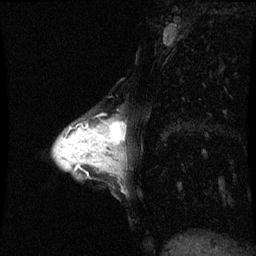
Breast MRI (dynamic contrast-enhanced), one sagittal slice; dynamic contrast-enhanced series, image 2 of 3 at this slice position (ordered by acquisition); 1.5 T; TE 4.2 ms, TR 8.9 ms; 256 × 256 image matrix, field of view 200 × 200 mm. Female patient, age 33 years. From the clinical record (not read from this slice): setting: breast cancer imaged before/during neoadjuvant chemotherapy; receptor status: HER2-positive.
Annotated regions visible in this slice (semi-automatically segmented with operator editing):
- analysis volume of interest (the breast-tissue region the enhancement analysis was run in; not a lesion): bounding box [x1, y1, x2, y2] px = [95, 120, 126, 153]
- tumour enhancement mask (voxels above the 70 % enhancement threshold inside the analysis volume of interest): [101, 122, 124, 145]